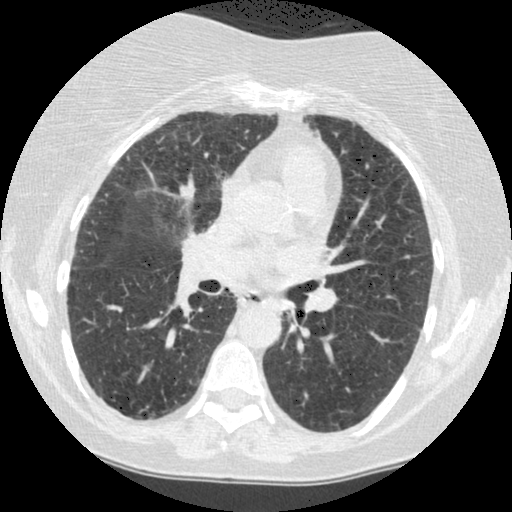
Chest CT (low-dose screening protocol), one axial image, baseline annual screen, lung window (W 1500 / L -600 HU), 1.25 mm slice thickness, standard (soft-tissue) reconstruction kernel (STANDARD), slice 204 of 442 in the series. Female participant, aged 60 years at enrolment. Former smoker at enrolment.
Expert-annotated lung lesion, bounding box (x1, y1, x2, y2) in pixels: (269, 292, 310, 334). The screening reader recorded 2 non-calcified nodules or masses ≥4 mm on this exam (right lower lobe, left lower lobe); which of them this box marks is not recorded. Official screen result: positive, change unspecified: nodule(s) >= 4 mm or enlarging nodule(s), mass(es), or other non-specific abnormalities suspicious for lung cancer. Lung cancer was diagnosed 794 days after this screen (after the third annual screen): small cell carcinoma, NOS, left lower lobe, undifferentiated (G4), stage IV (AJCC 6th edition), 69 mm at pathology.